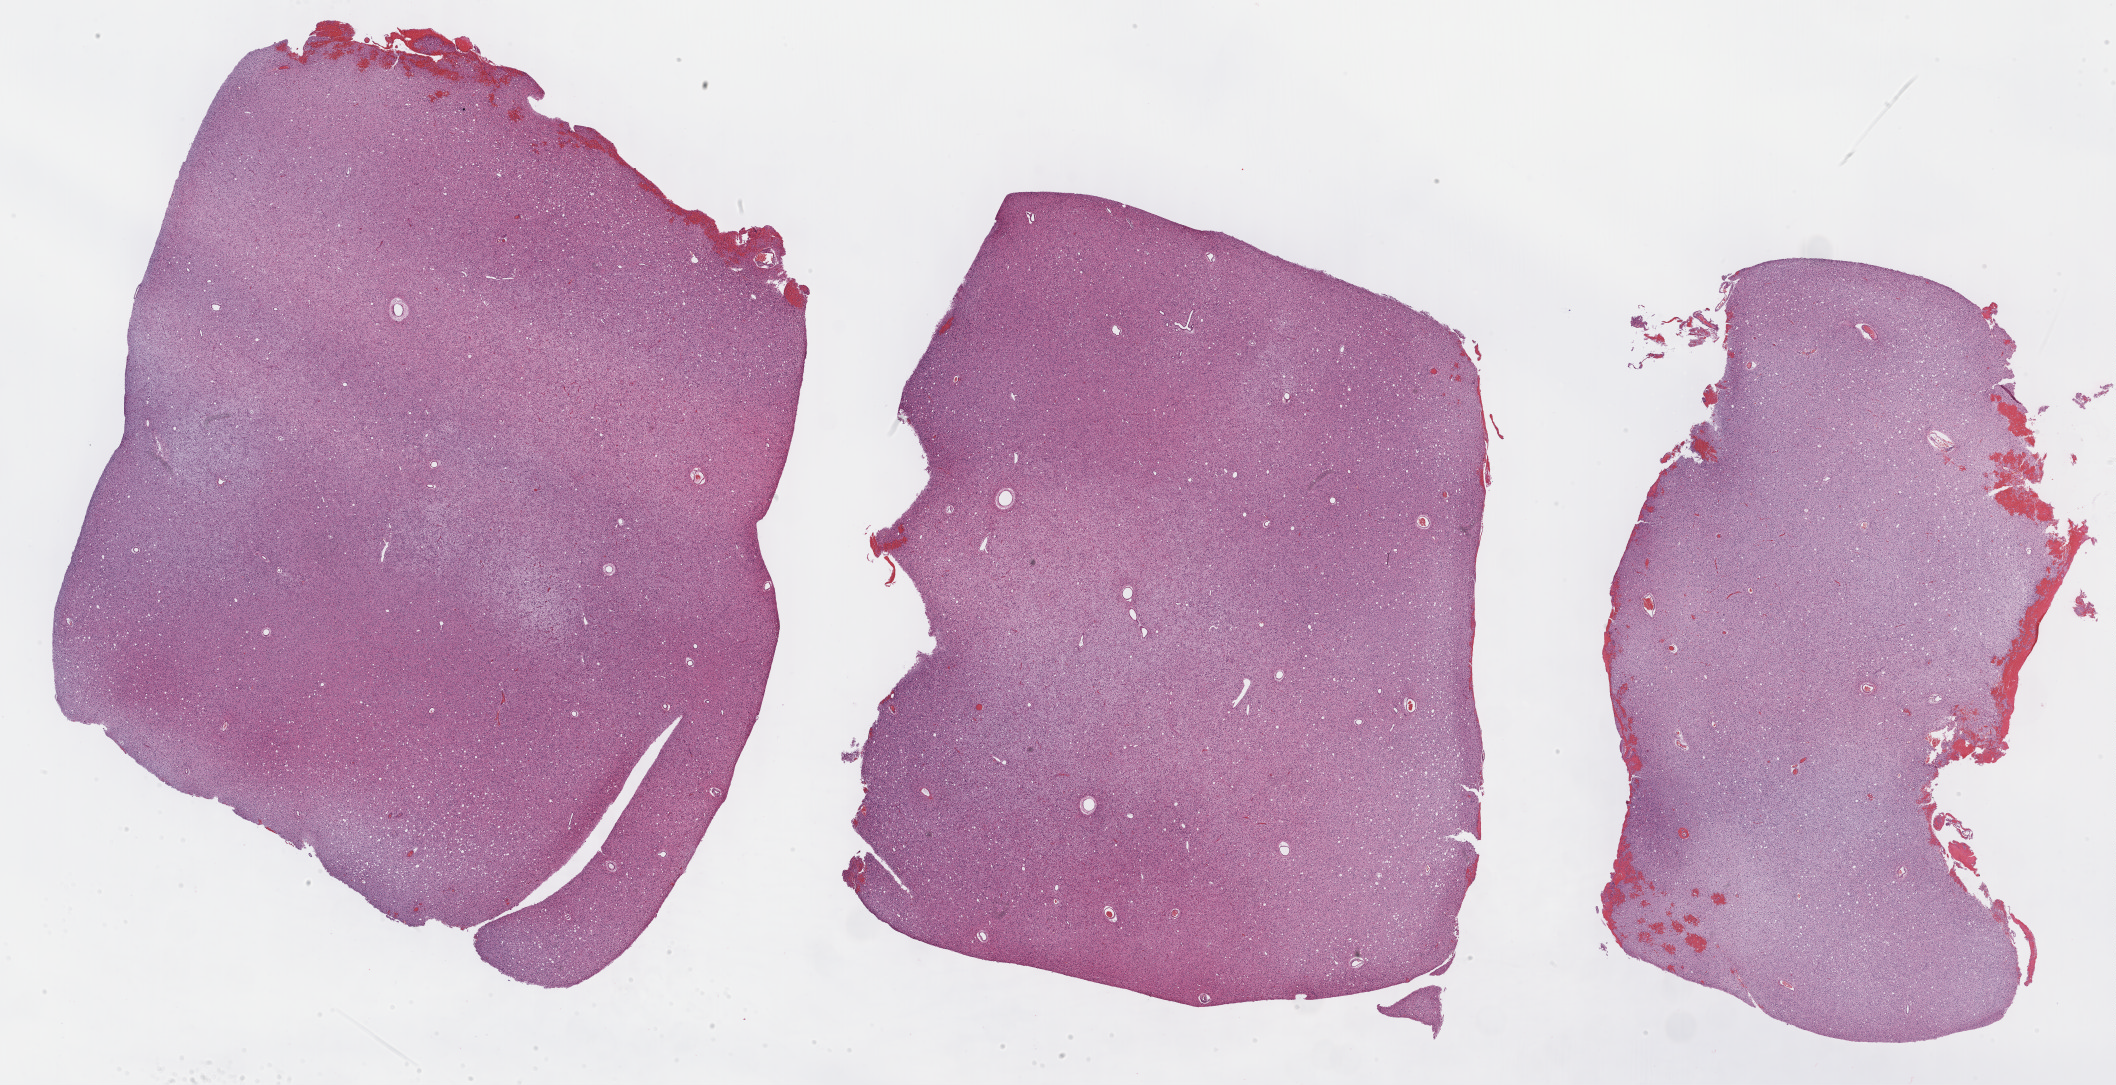
Hematoxylin and eosin (H&E) stained whole-slide image, shown as a low-resolution overview of the whole scanned area (about 34.2 x 17.6 mm), FFPE section, sample: primary tumour, brain. Female, age 24 years at initial diagnosis. Histologic grade: G2 (moderately differentiated).
- pathologic diagnosis: Astrocytoma, NOS (cerebrum)